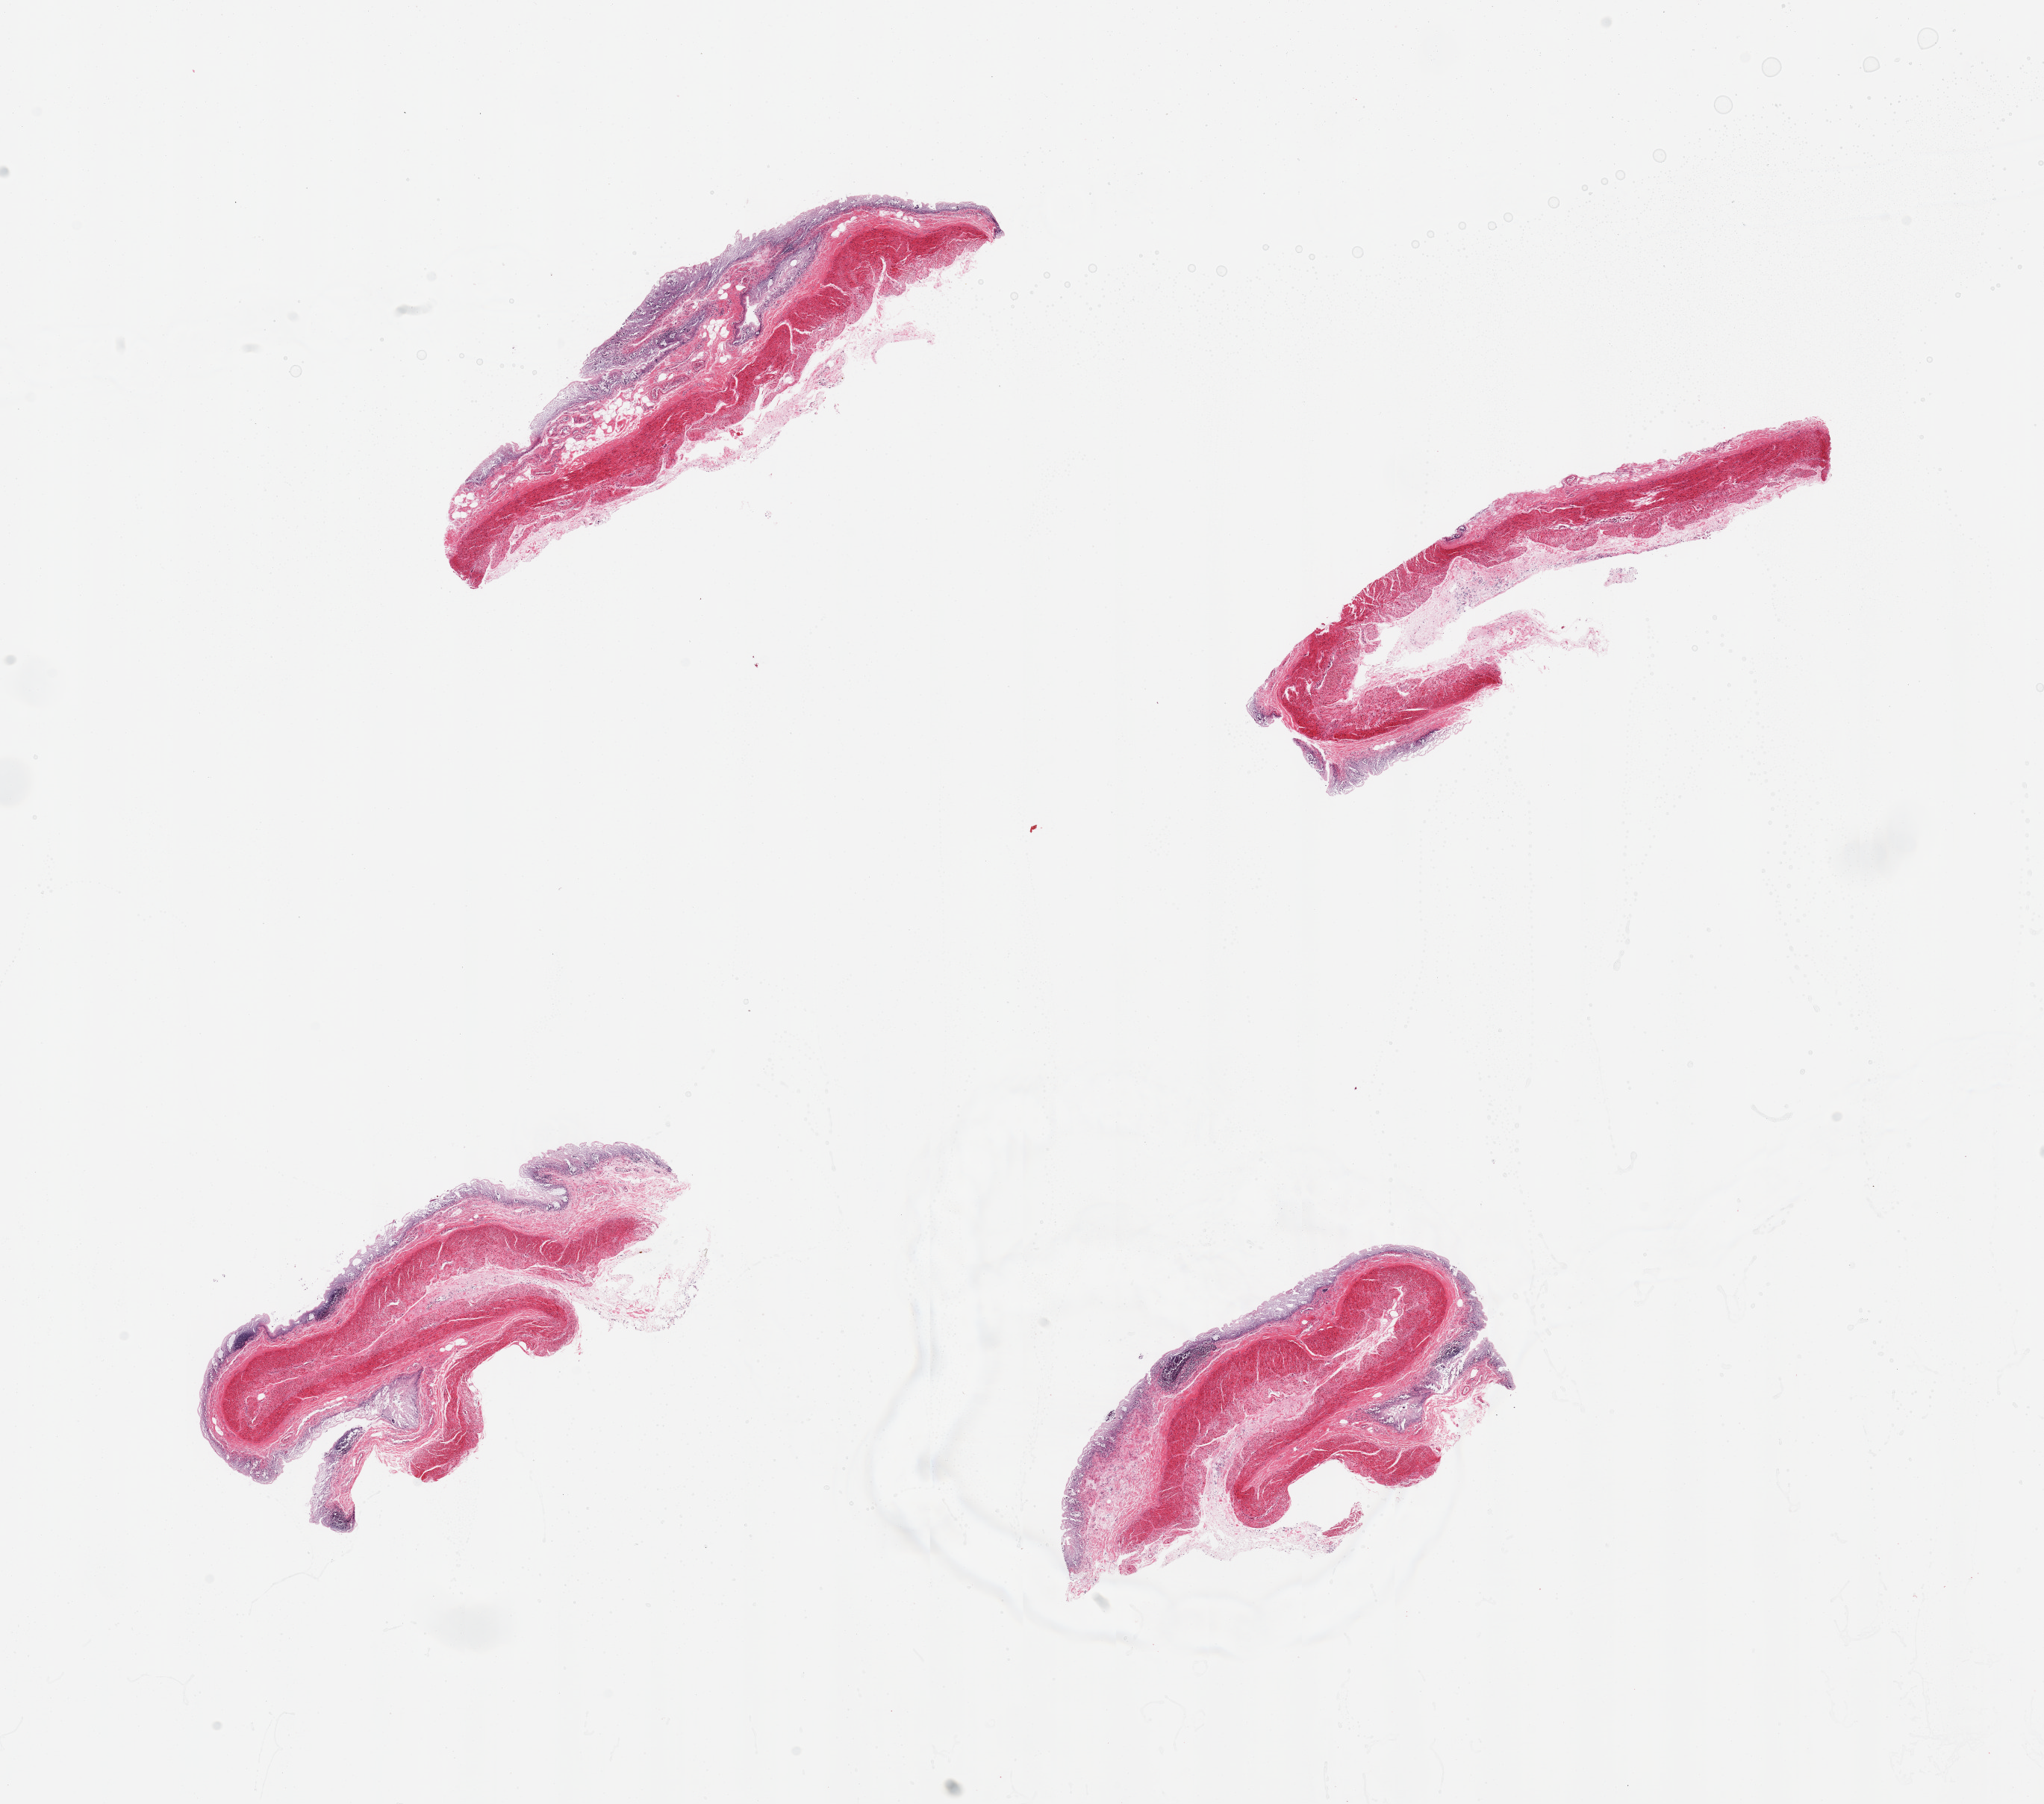
Digitized H&E-stained section — a low-resolution overview of the entire scanned area, about 21.7 x 19.1 mm. PAXgene-fixed paraffin-embedded (PFPE) section. Section of transverse colon (target tissue). Tissue donor sample. Male donor.
Pathologist's review note for this sample: 4 pieces; full thickness sections with severely autolyzed mucosa, discontinuous in one piece.